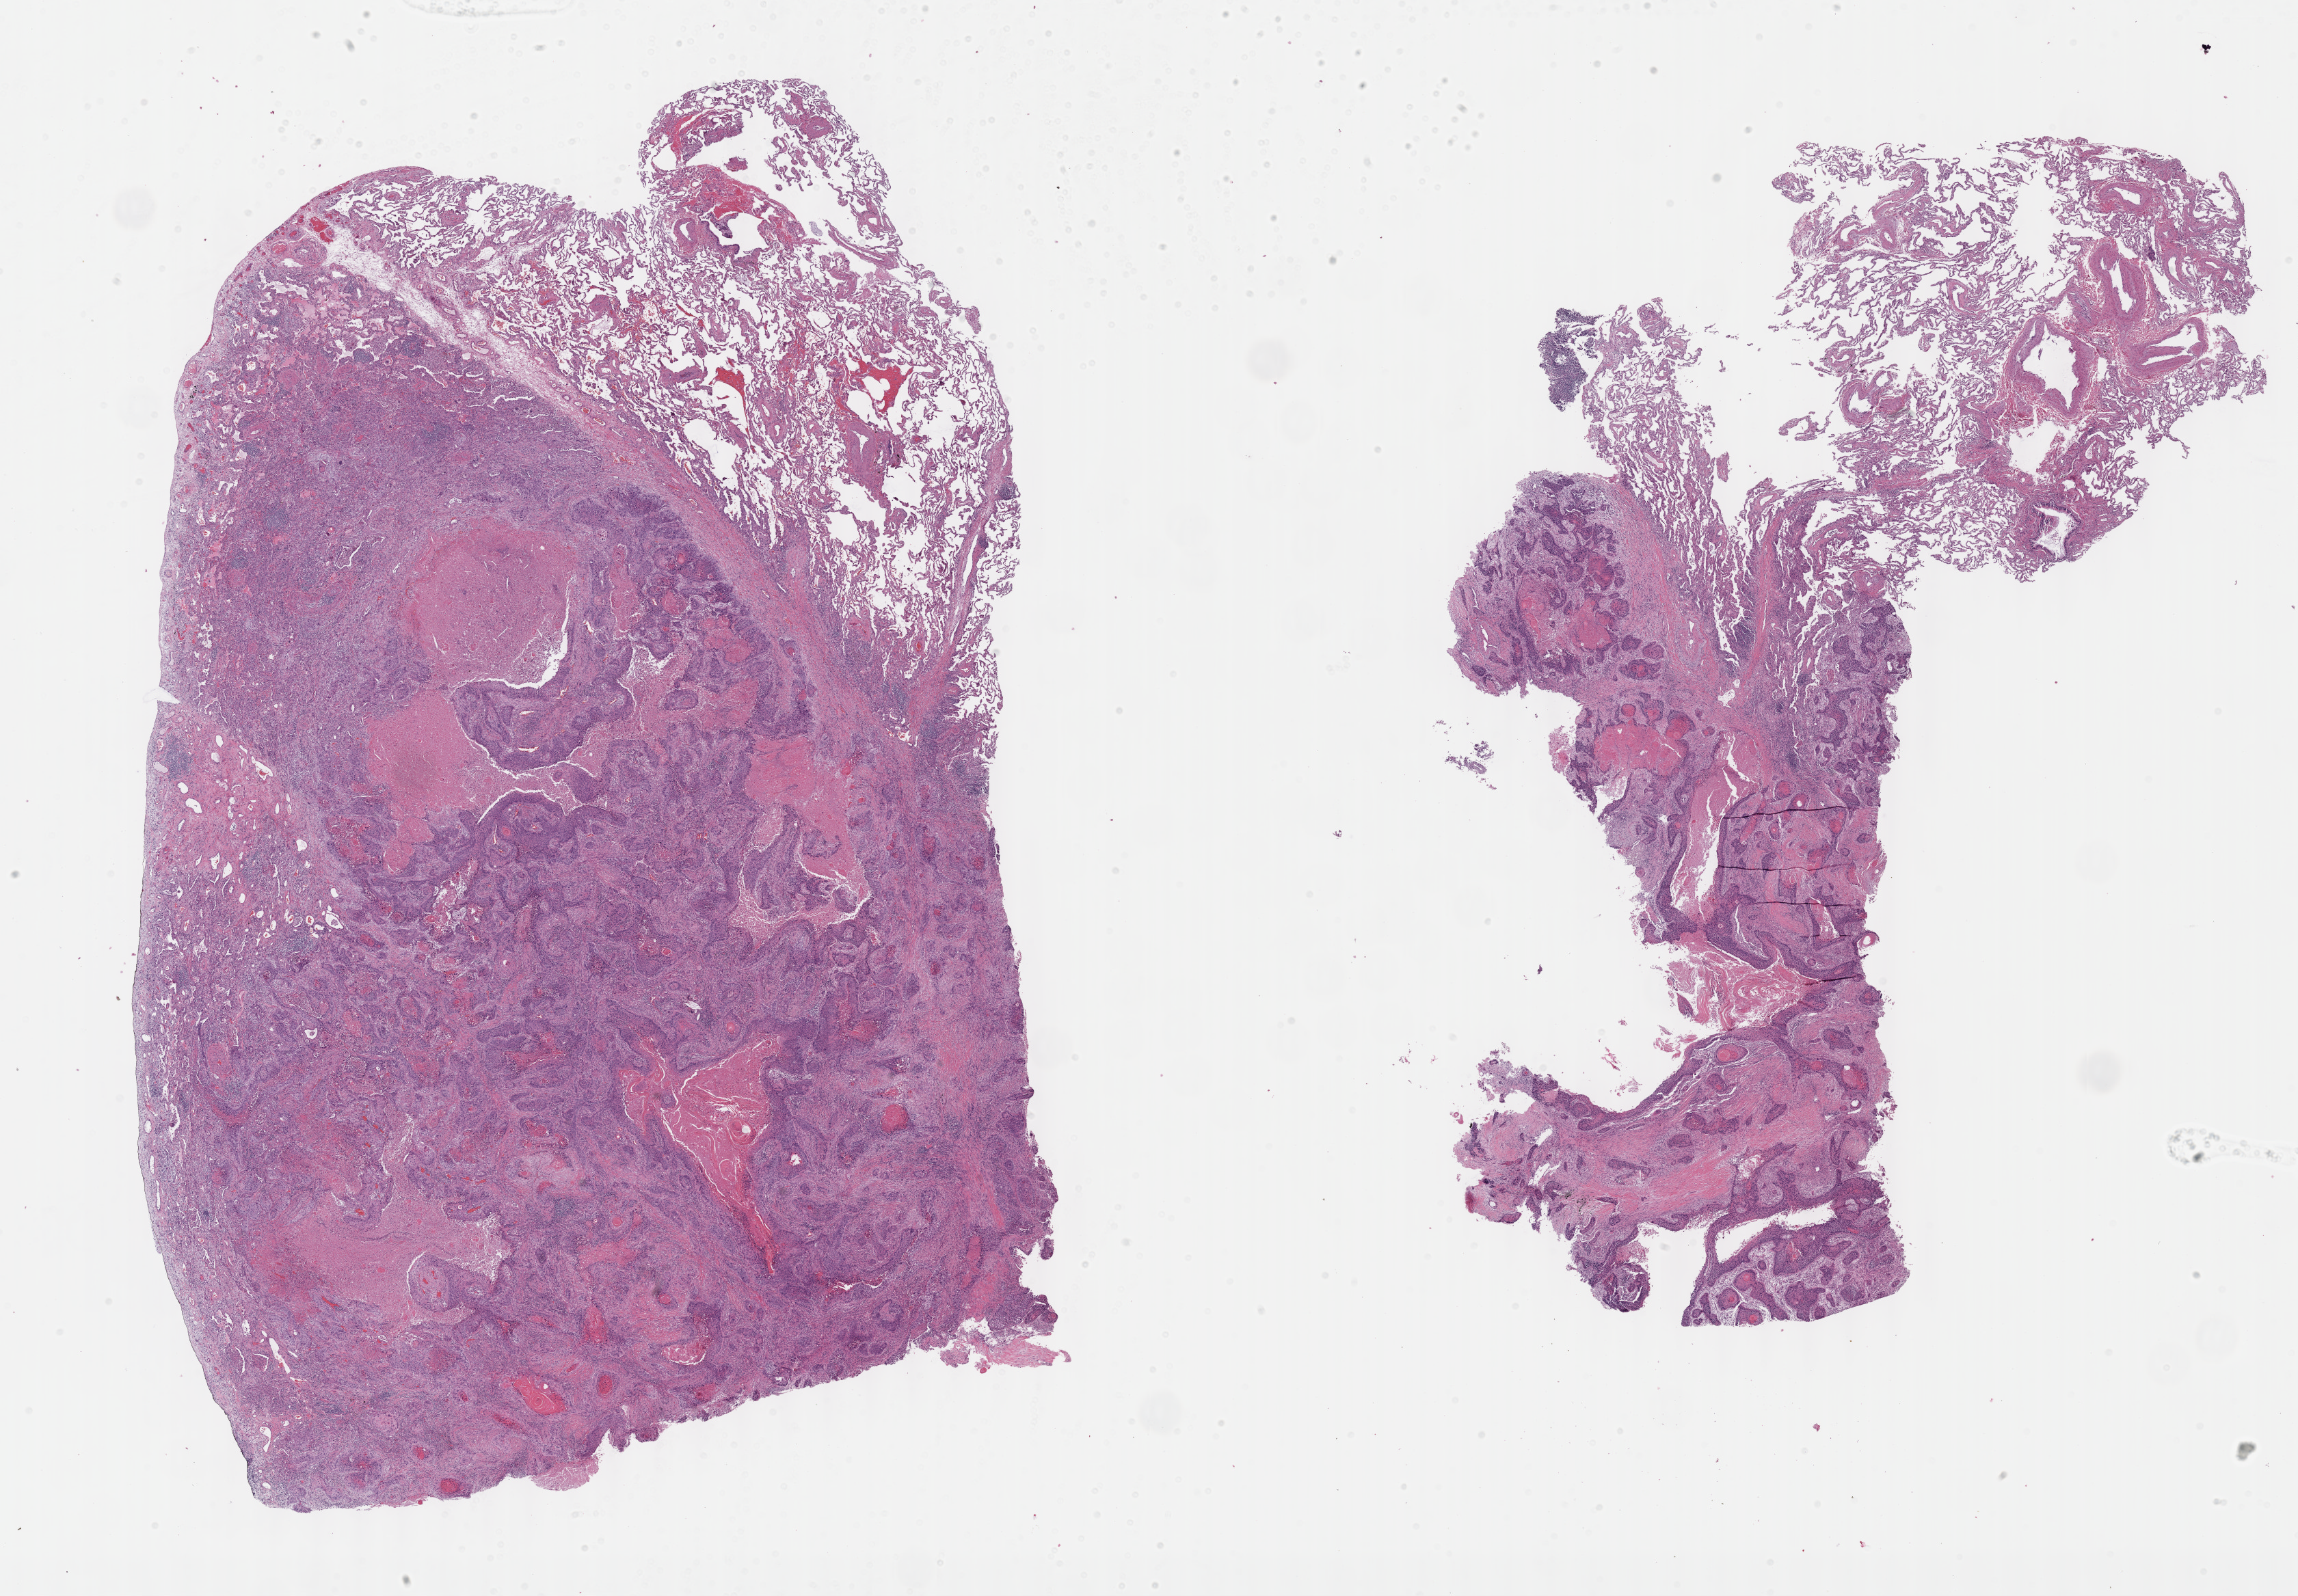
Whole-slide histology image, Hematoxylin and eosin (H&E) stained — a low-resolution overview of the entire scanned area, about 27.2 x 18.9 mm (slide scanned at 40x). FFPE section. Sample: primary tumour, lung. Male, age 81 years at initial diagnosis.
Pathologic diagnosis: Squamous cell carcinoma, NOS (upper lobe, lung).